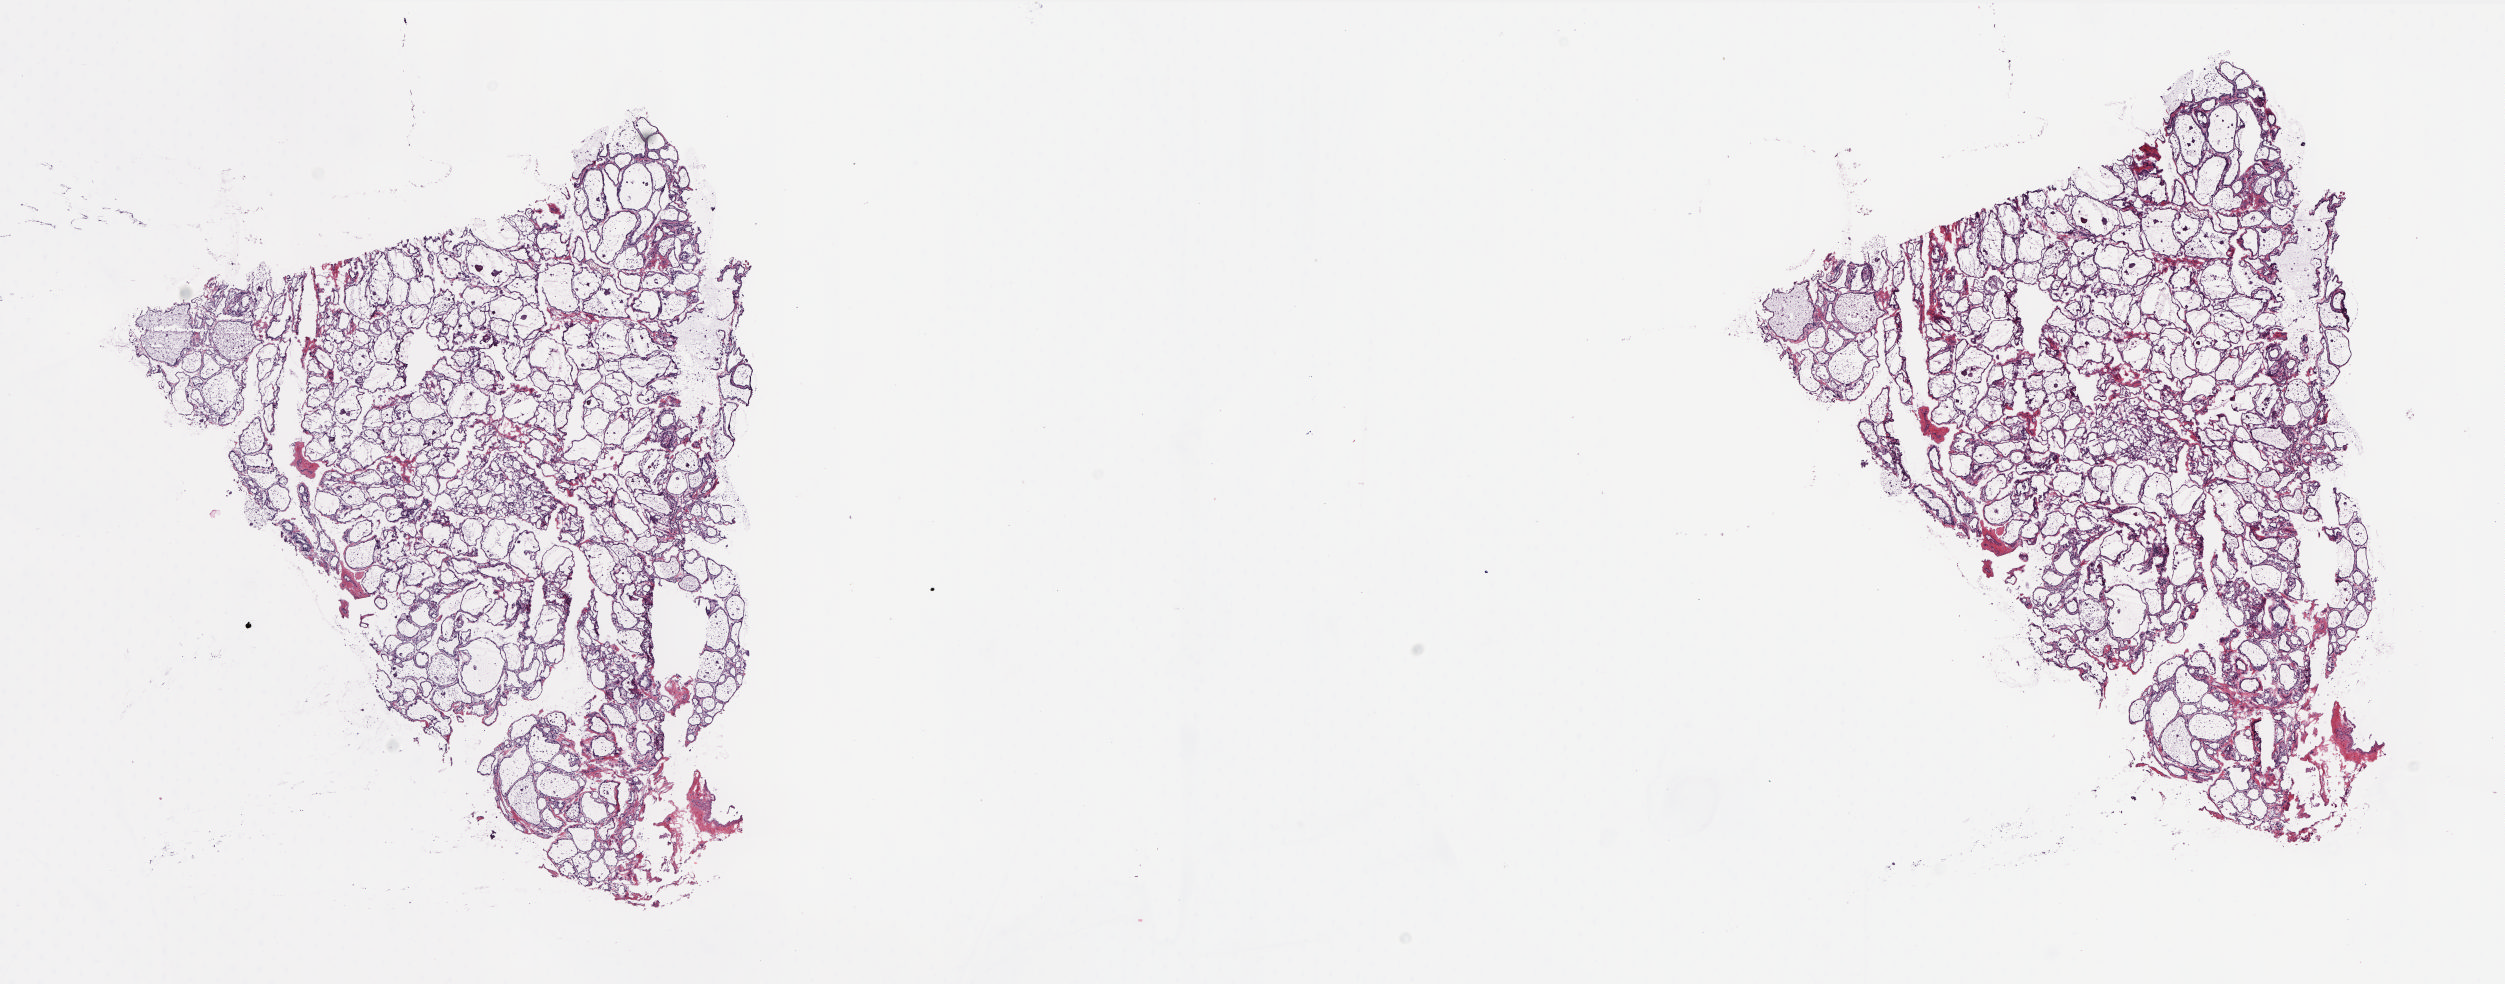
H&E whole-slide image — shown as a low-resolution overview of the whole scanned area (about 20.2 x 7.9 mm). Frozen section from the top of the tissue portion. Sample: solid tissue normal (non-tumour tissue), thyroid. Male, age 41 years at initial diagnosis. Slide review estimates, as recorded: tumour cells 0%, tumour nuclei 0%, normal cells 100%, stromal cells 0%, necrosis 0%. Infiltration values recorded for this section: lymphocyte infiltration 2%, monocyte infiltration 3%, neutrophil infiltration 0%.
This section: solid tissue normal sample (biorepository sample class). Patient diagnosis: Papillary adenocarcinoma, NOS (thyroid gland).